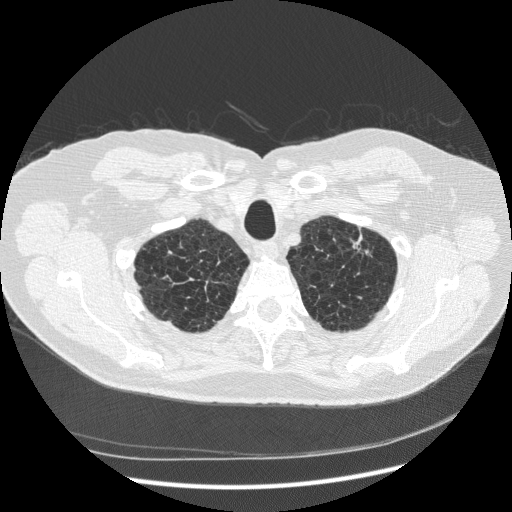
Axial slice from a low-dose chest CT screening exam; baseline annual screen; lung window (W 1500 / L -600 HU); 1.25 mm slice thickness; 512 × 512 image matrix, field of view 380 × 380 mm. Male, age 70 years at enrolment. Former smoker at enrolment.
- Expert reader's lesion annotation, bounding box <333,221,389,277> (left, top, right, bottom; pixels).
- The screening reader recorded 2 non-calcified nodules or masses ≥4 mm on this exam; which of them this box marks is not recorded.
- Official screen result: positive, change unspecified: nodule(s) >= 4 mm or enlarging nodule(s), mass(es), or other non-specific abnormalities suspicious for lung cancer.
- Later outcome: lung cancer diagnosed 816 days after this screen (after the third annual screen) — squamous cell carcinoma, NOS, left upper lobe, moderately differentiated (G2), stage IA (AJCC 6th edition), 18 mm at pathology.